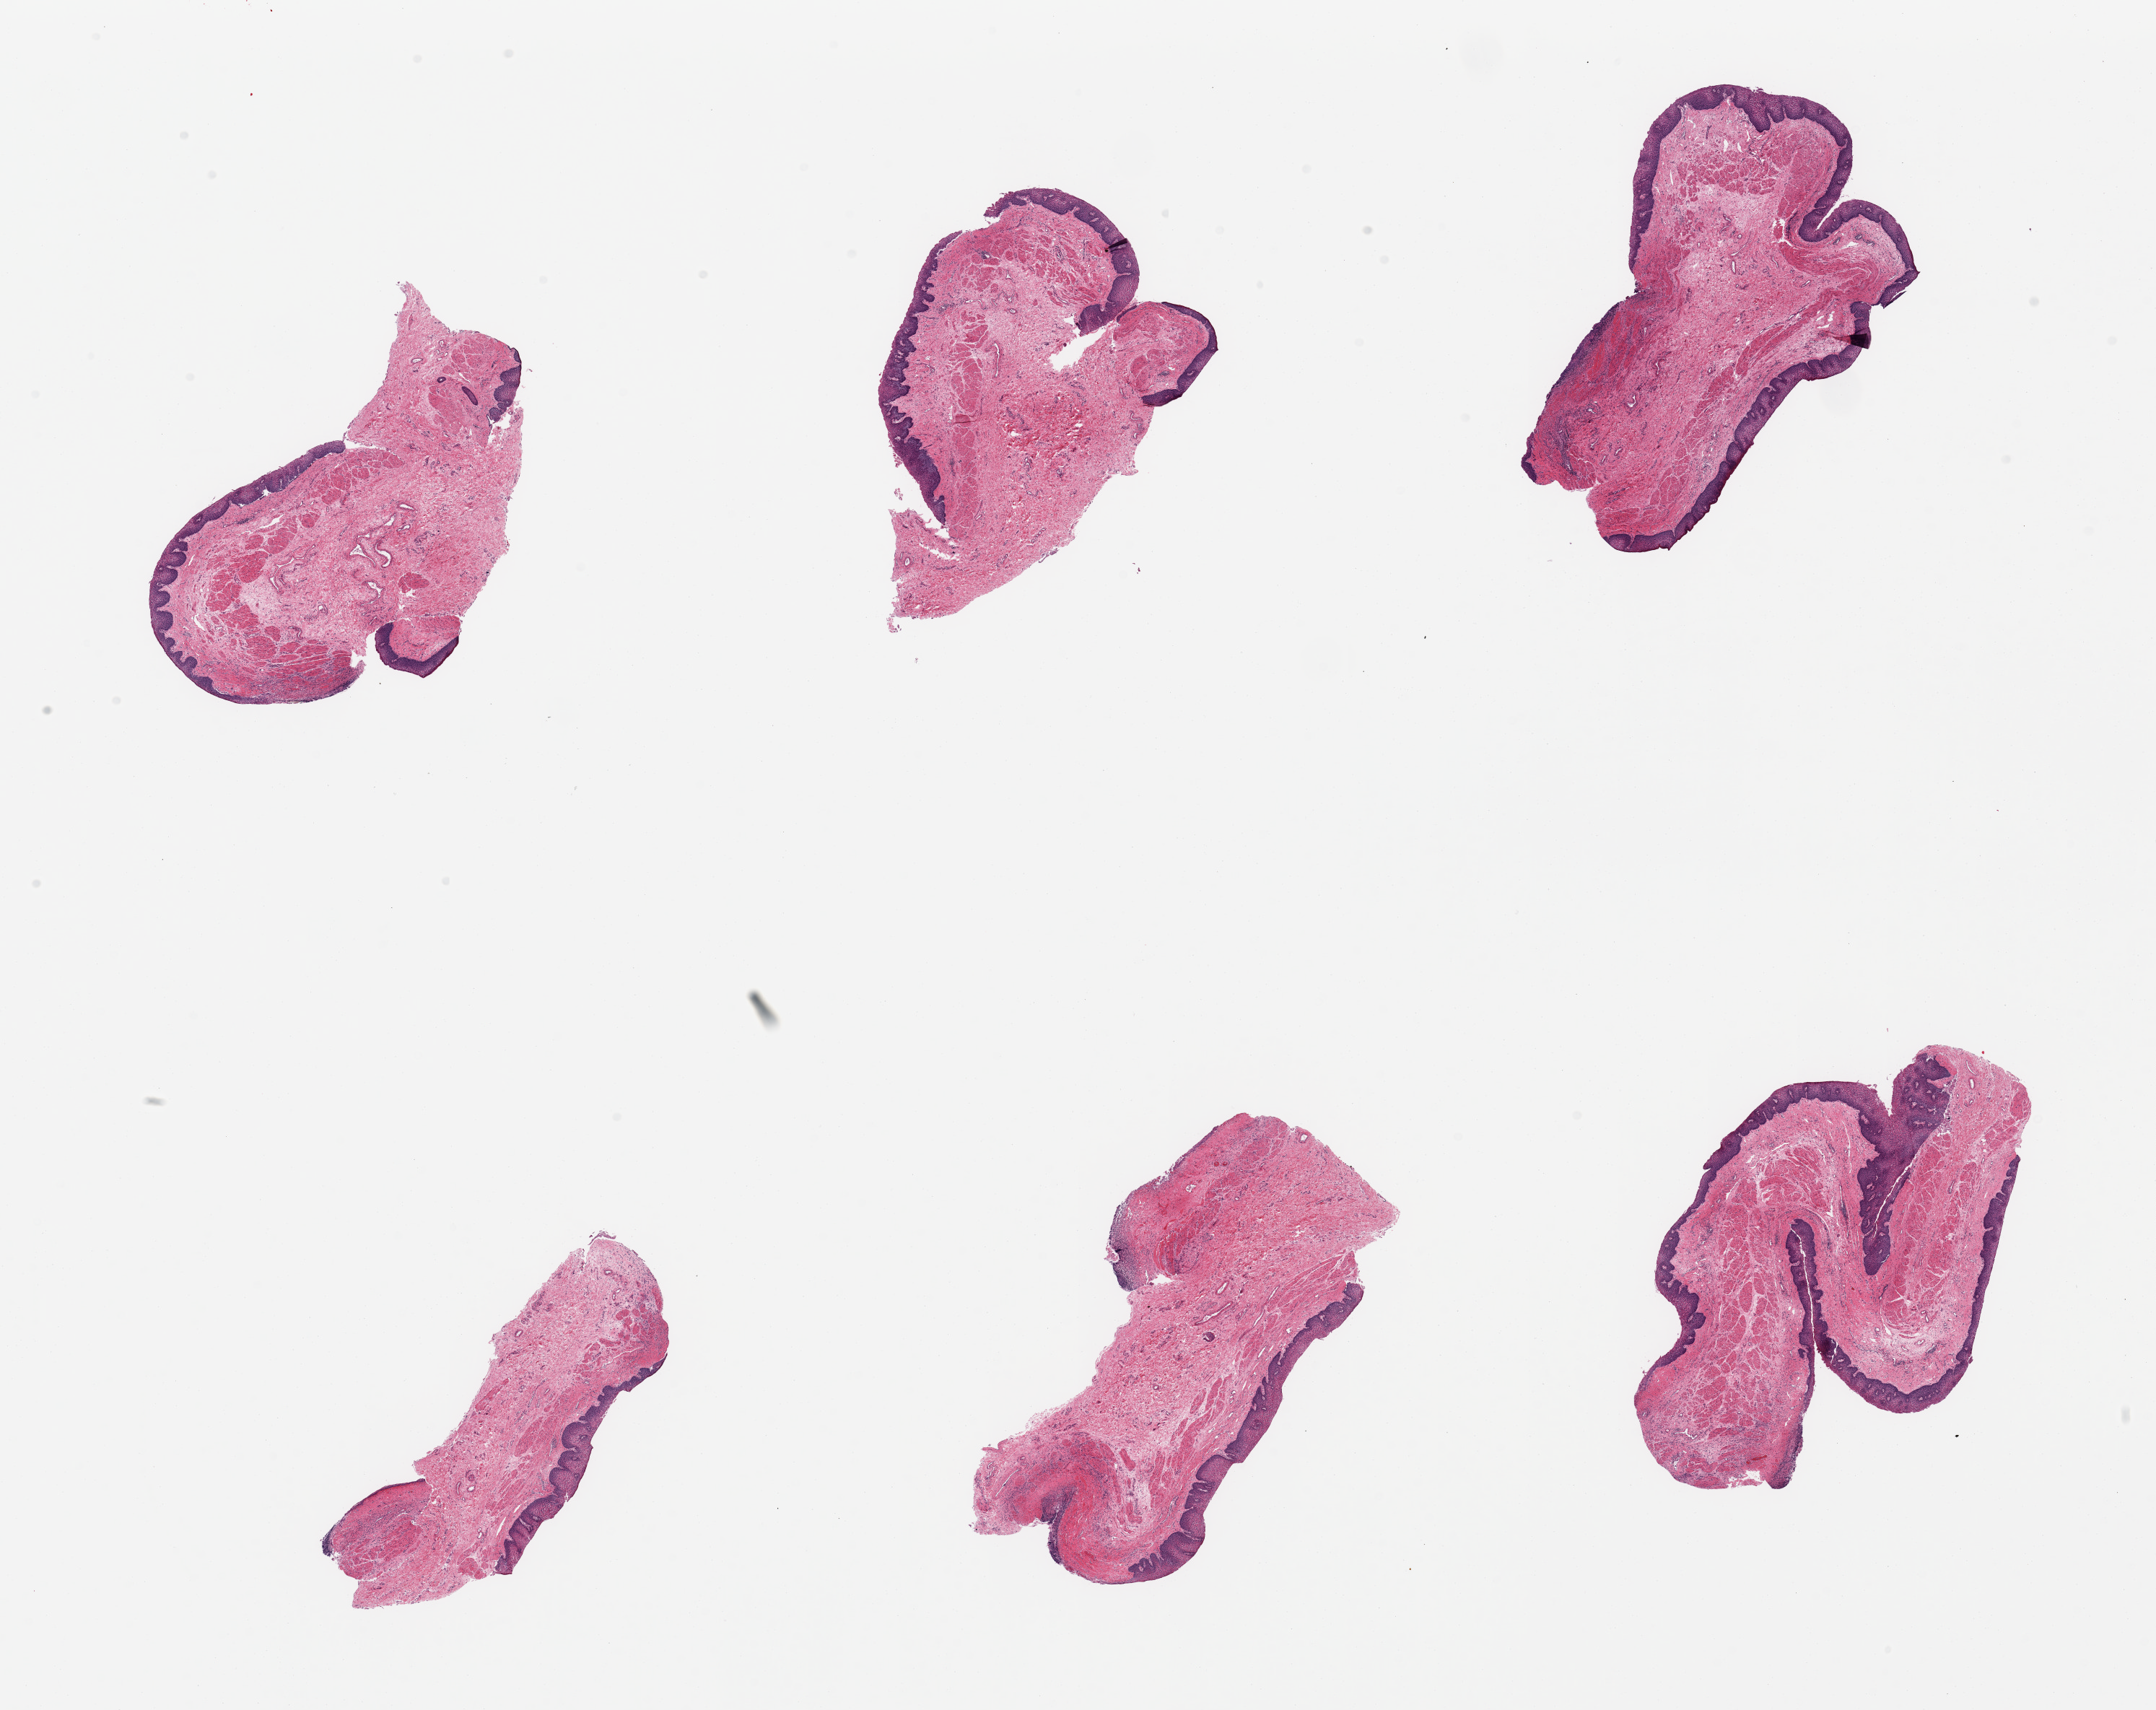
Digitized H&E-stained section, low-resolution overview of the scanned area, about 23.6 x 18.7 mm, PAXgene-fixed, paraffin-embedded tissue, target tissue: esophageal mucous membrane, donor tissue sample.
Review note (as recorded): 6 pieces; well dissected squamous mucosa.